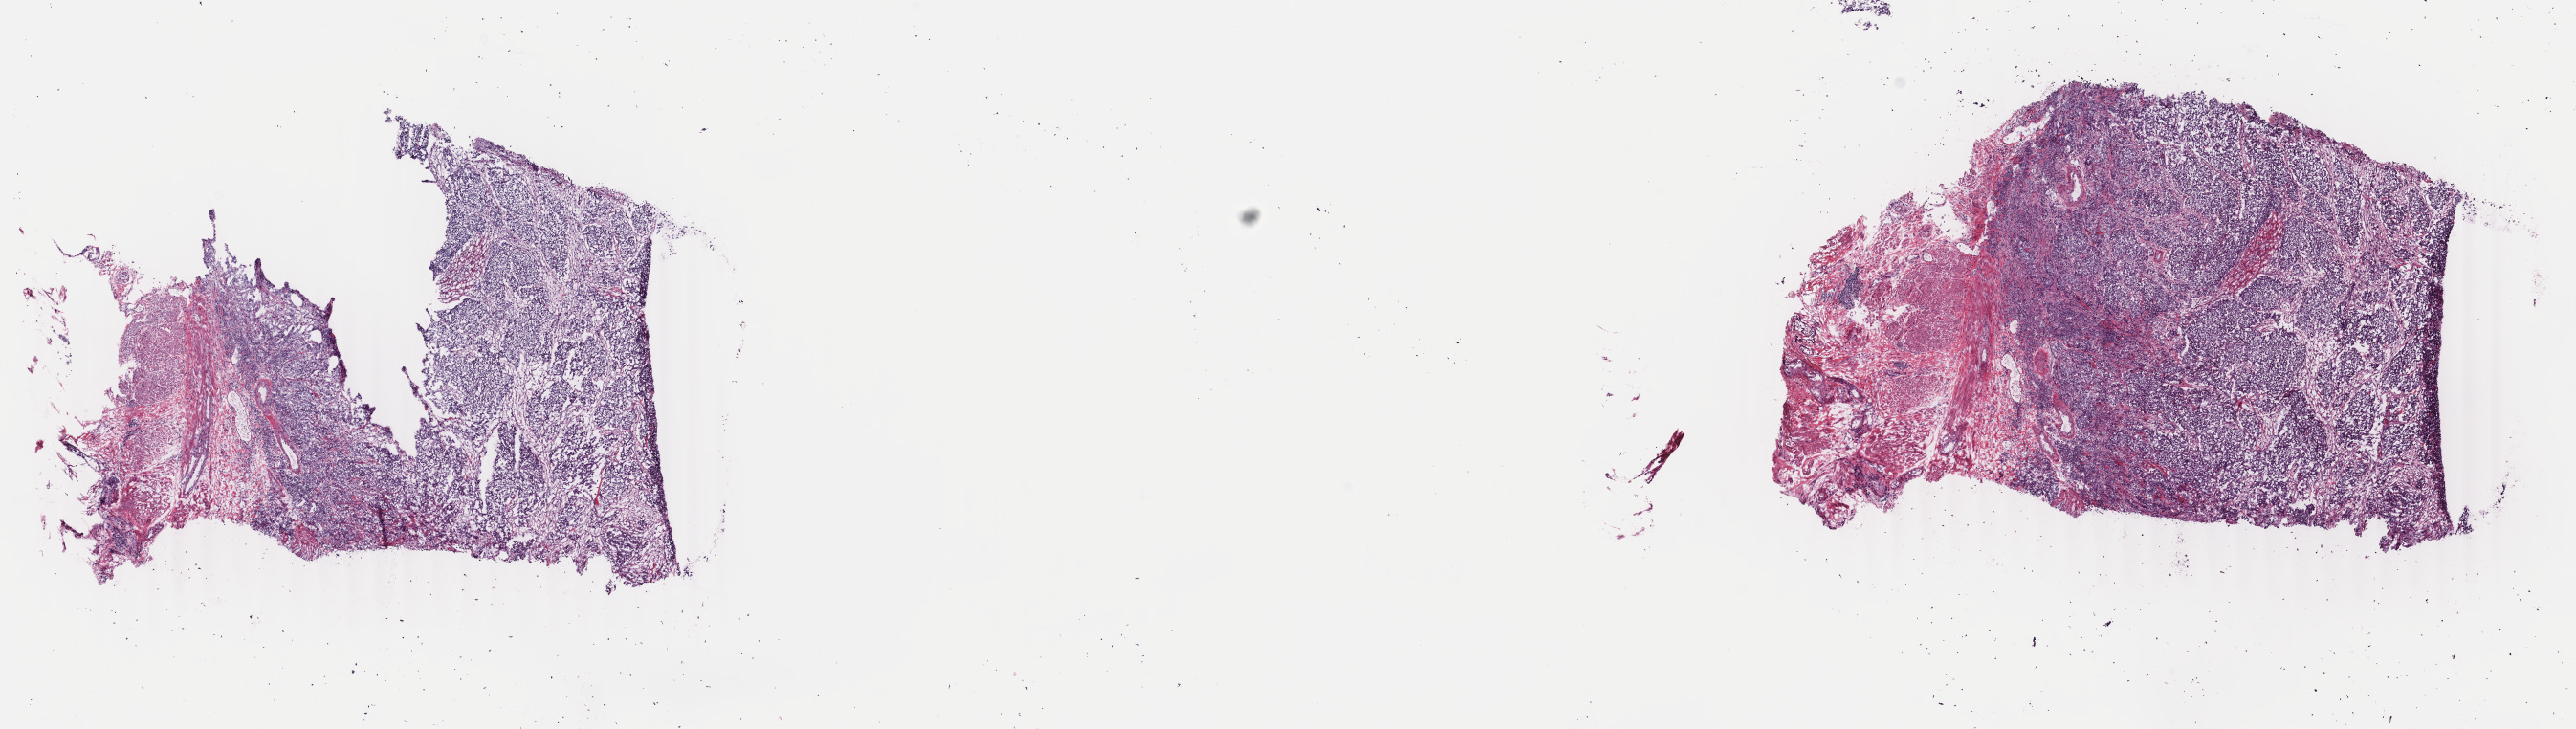
Digitized H&E-stained tissue section (whole slide) — shown as a low-resolution overview of the whole scanned area (about 21.4 x 6.1 mm). Frozen section. Primary tumour sample from the bladder. Female patient; age at initial diagnosis 73 years. Histologic grade: high grade. Slide review estimates, as recorded: tumour cells 70%, tumour nuclei 70%, normal cells 0%, stromal cells 30%, necrosis 0%. Inflammatory infiltration, as recorded: lymphocyte infiltration 5%, monocyte infiltration 0%, neutrophil infiltration 0%.
AJCC pathologic stage: II. Histologic diagnosis: Papillary transitional cell carcinoma.